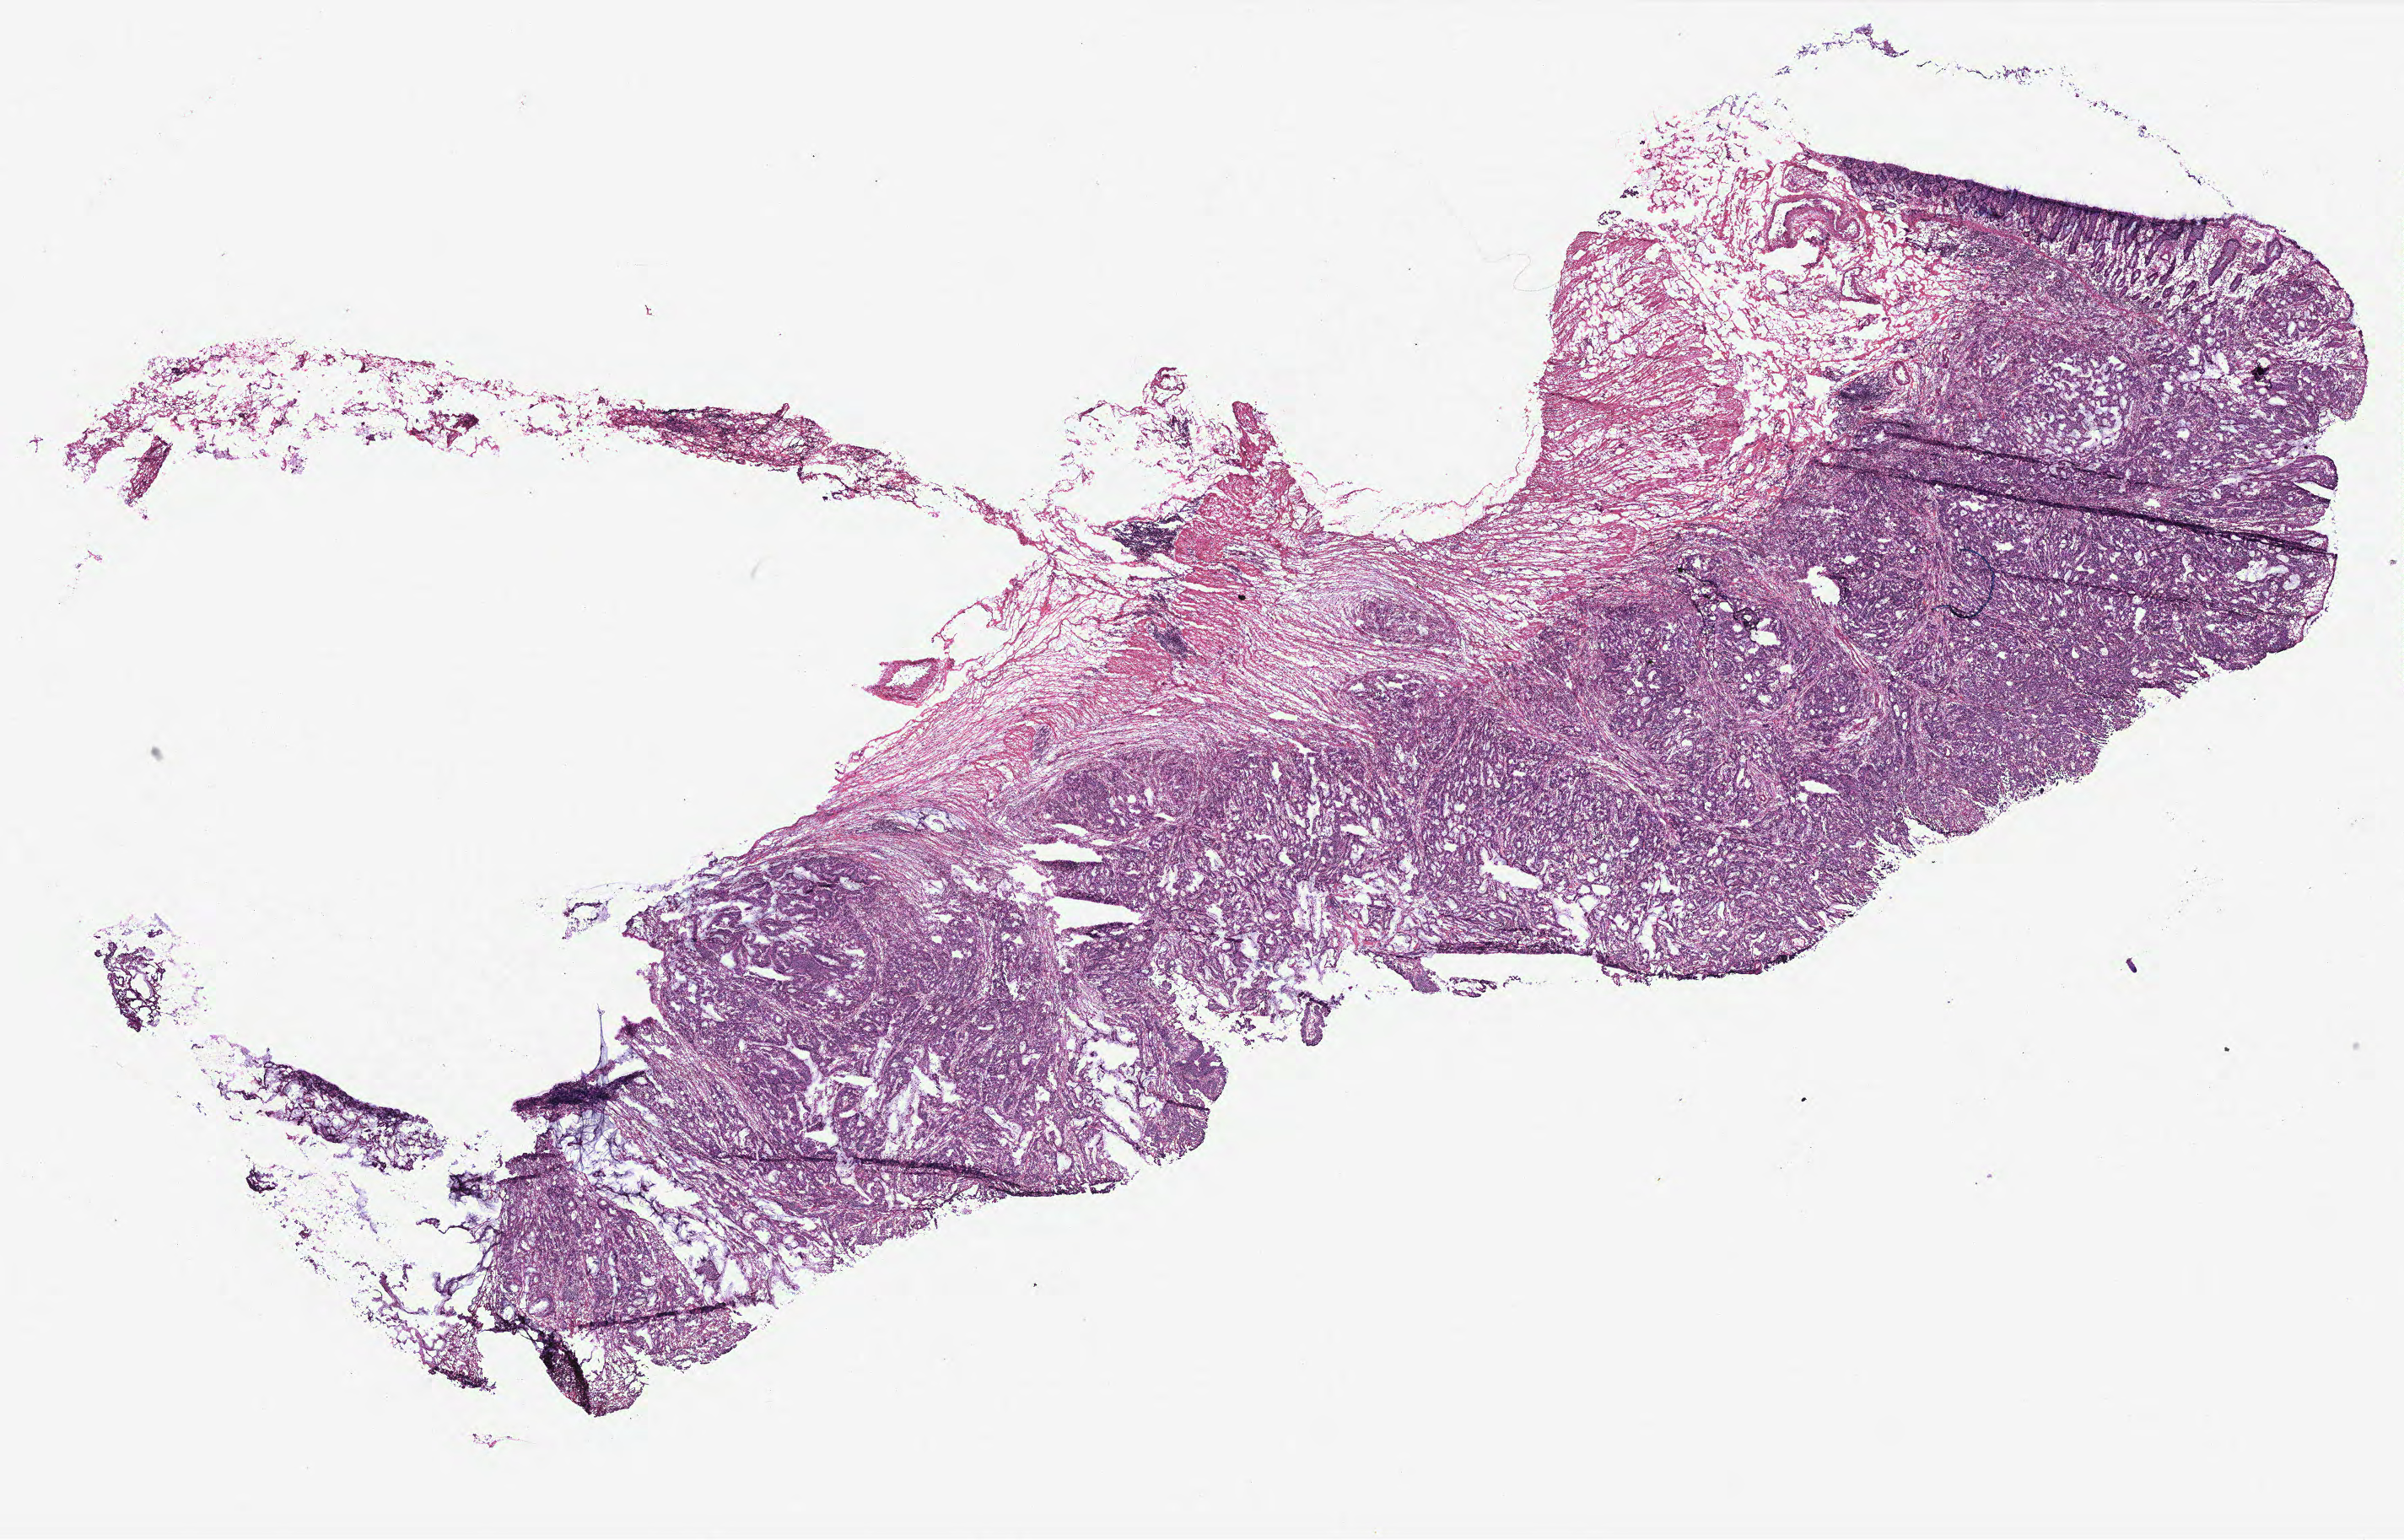
Digitized H&E tissue section (whole slide), a low-resolution overview of the entire scanned area, about 22.8 x 14.6 mm (from a 40x scan); colon, normal (non-tumour) tissue. 61-year-old female patient.
This section: normal (non-tumour) tissue from the same patient. Patient diagnosis: Adenocarcinoma, NOS.